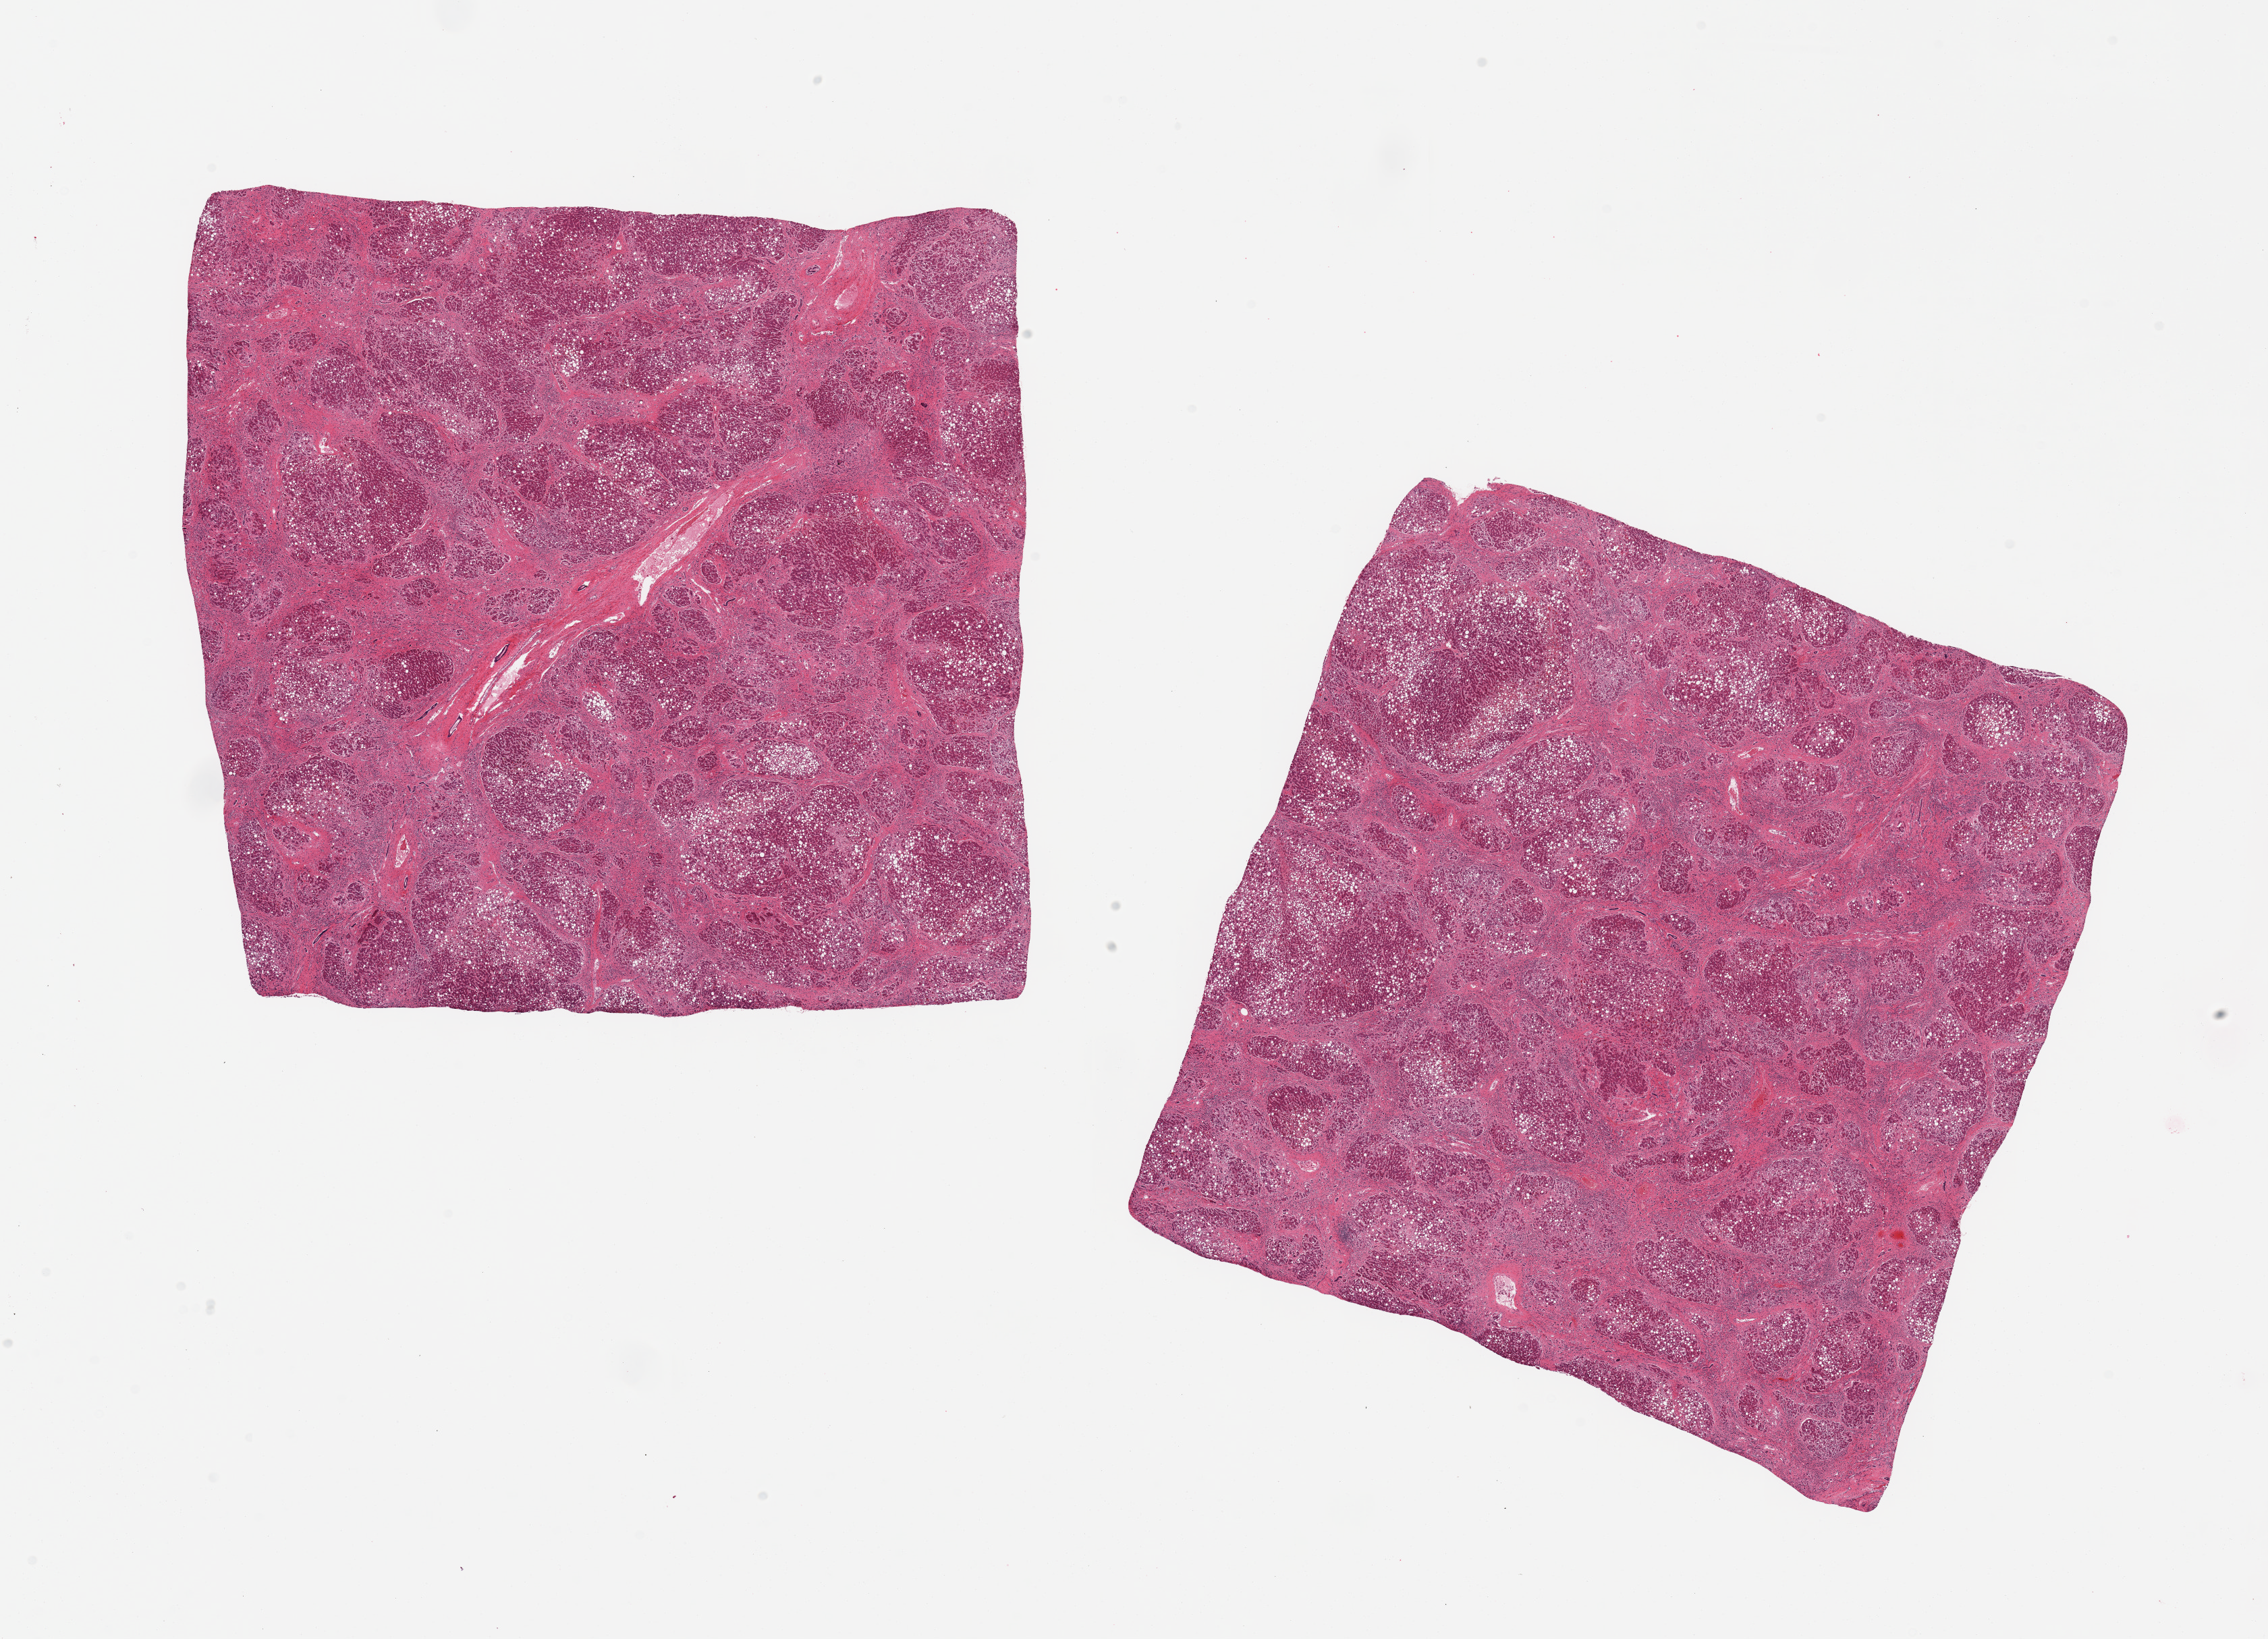
Digitized haematoxylin and eosin-stained section, a low-resolution overview of the entire scanned area, about 26.6 x 19.2 mm (slide scanned at 20x), PAXgene-fixed, paraffin-embedded tissue, target tissue: liver, donor tissue sample. Donor: male.
Review note (as recorded): 2 pieces; nodular cirrhosis, alcoholic hyalin (Mallory bodies) with 50% macrosteatosis.